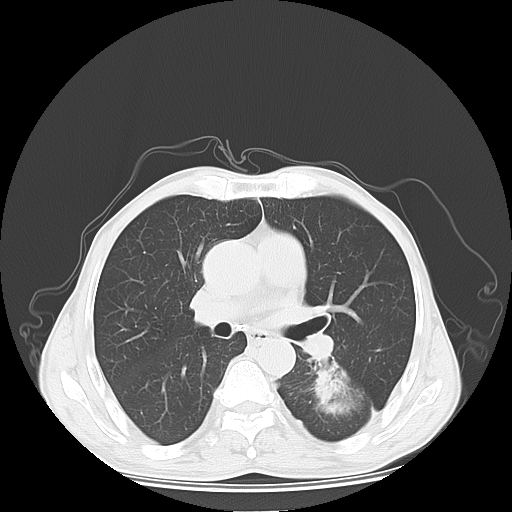
Chest CT, one axial slice; slice 36 of 65 in the series (ordered by position); reconstruction kernel LUNG; lung window (W 1500 / L -600 HU); 512 × 512 image matrix, field of view 350 × 350 mm. Patient: male, 63 years. Case-level facts recorded for this patient, not image findings: clinical TNM (as recorded): T1c N0 M1b.
Outlined on this slice (rectangle marked by the reading radiologist):
- lung tumour (recorded histology: adenocarcinoma): bounding box (x1, y1, x2, y2) in pixels: (312, 360, 369, 420)